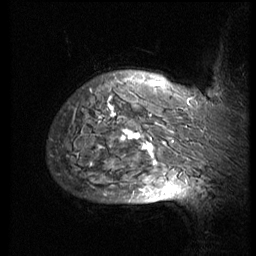
Breast MRI (dynamic contrast-enhanced), one sagittal slice. Position 62 of 74 along the scan axis. 3 images stored at this slice position (order not interpretable as contrast timing). 1.5 T. TE 4.2 ms, TR 8.9 ms. 2.5 mm slice thickness. 256 × 256 image matrix, field of view 200 × 200 mm. Patient: female, 57 years. From the clinical record (not read from this slice): setting: breast cancer imaged before/during neoadjuvant chemotherapy; receptor status: HER2-positive.
Structures marked on this image (semi-automatically segmented with operator editing):
- analysis volume of interest (the breast-tissue region the enhancement analysis was run in; not a lesion): bounding box <51,67,248,173> (left, top, right, bottom; pixels)
- tumour enhancement mask (voxels above the 140 % enhancement threshold inside the analysis volume of interest): <100,84,194,165>